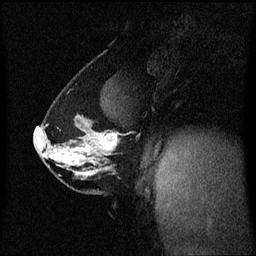
Breast MRI (dynamic contrast-enhanced), one sagittal slice; slice 36 of 60 in the series (ordered by position); dynamic contrast-enhanced series, image 2 of 3 at this slice position (ordered by acquisition); 1.5 T; TE 4.2 ms, TR 8.4 ms; 2 mm slice thickness; 256 × 256 image matrix. Patient: female, 40 years. Case-level facts recorded for this patient, not image findings: setting: breast cancer imaged before/during neoadjuvant chemotherapy; receptor status: triple-negative.
Structures marked on this image (semi-automatically segmented with operator editing):
- analysis volume of interest (the breast-tissue region the enhancement analysis was run in; not a lesion): box from (x=34, y=116) to (x=121, y=188) px
- tumour enhancement mask (voxels above the 70 % enhancement threshold inside the analysis volume of interest): (x=36, y=128)–(x=118, y=162)